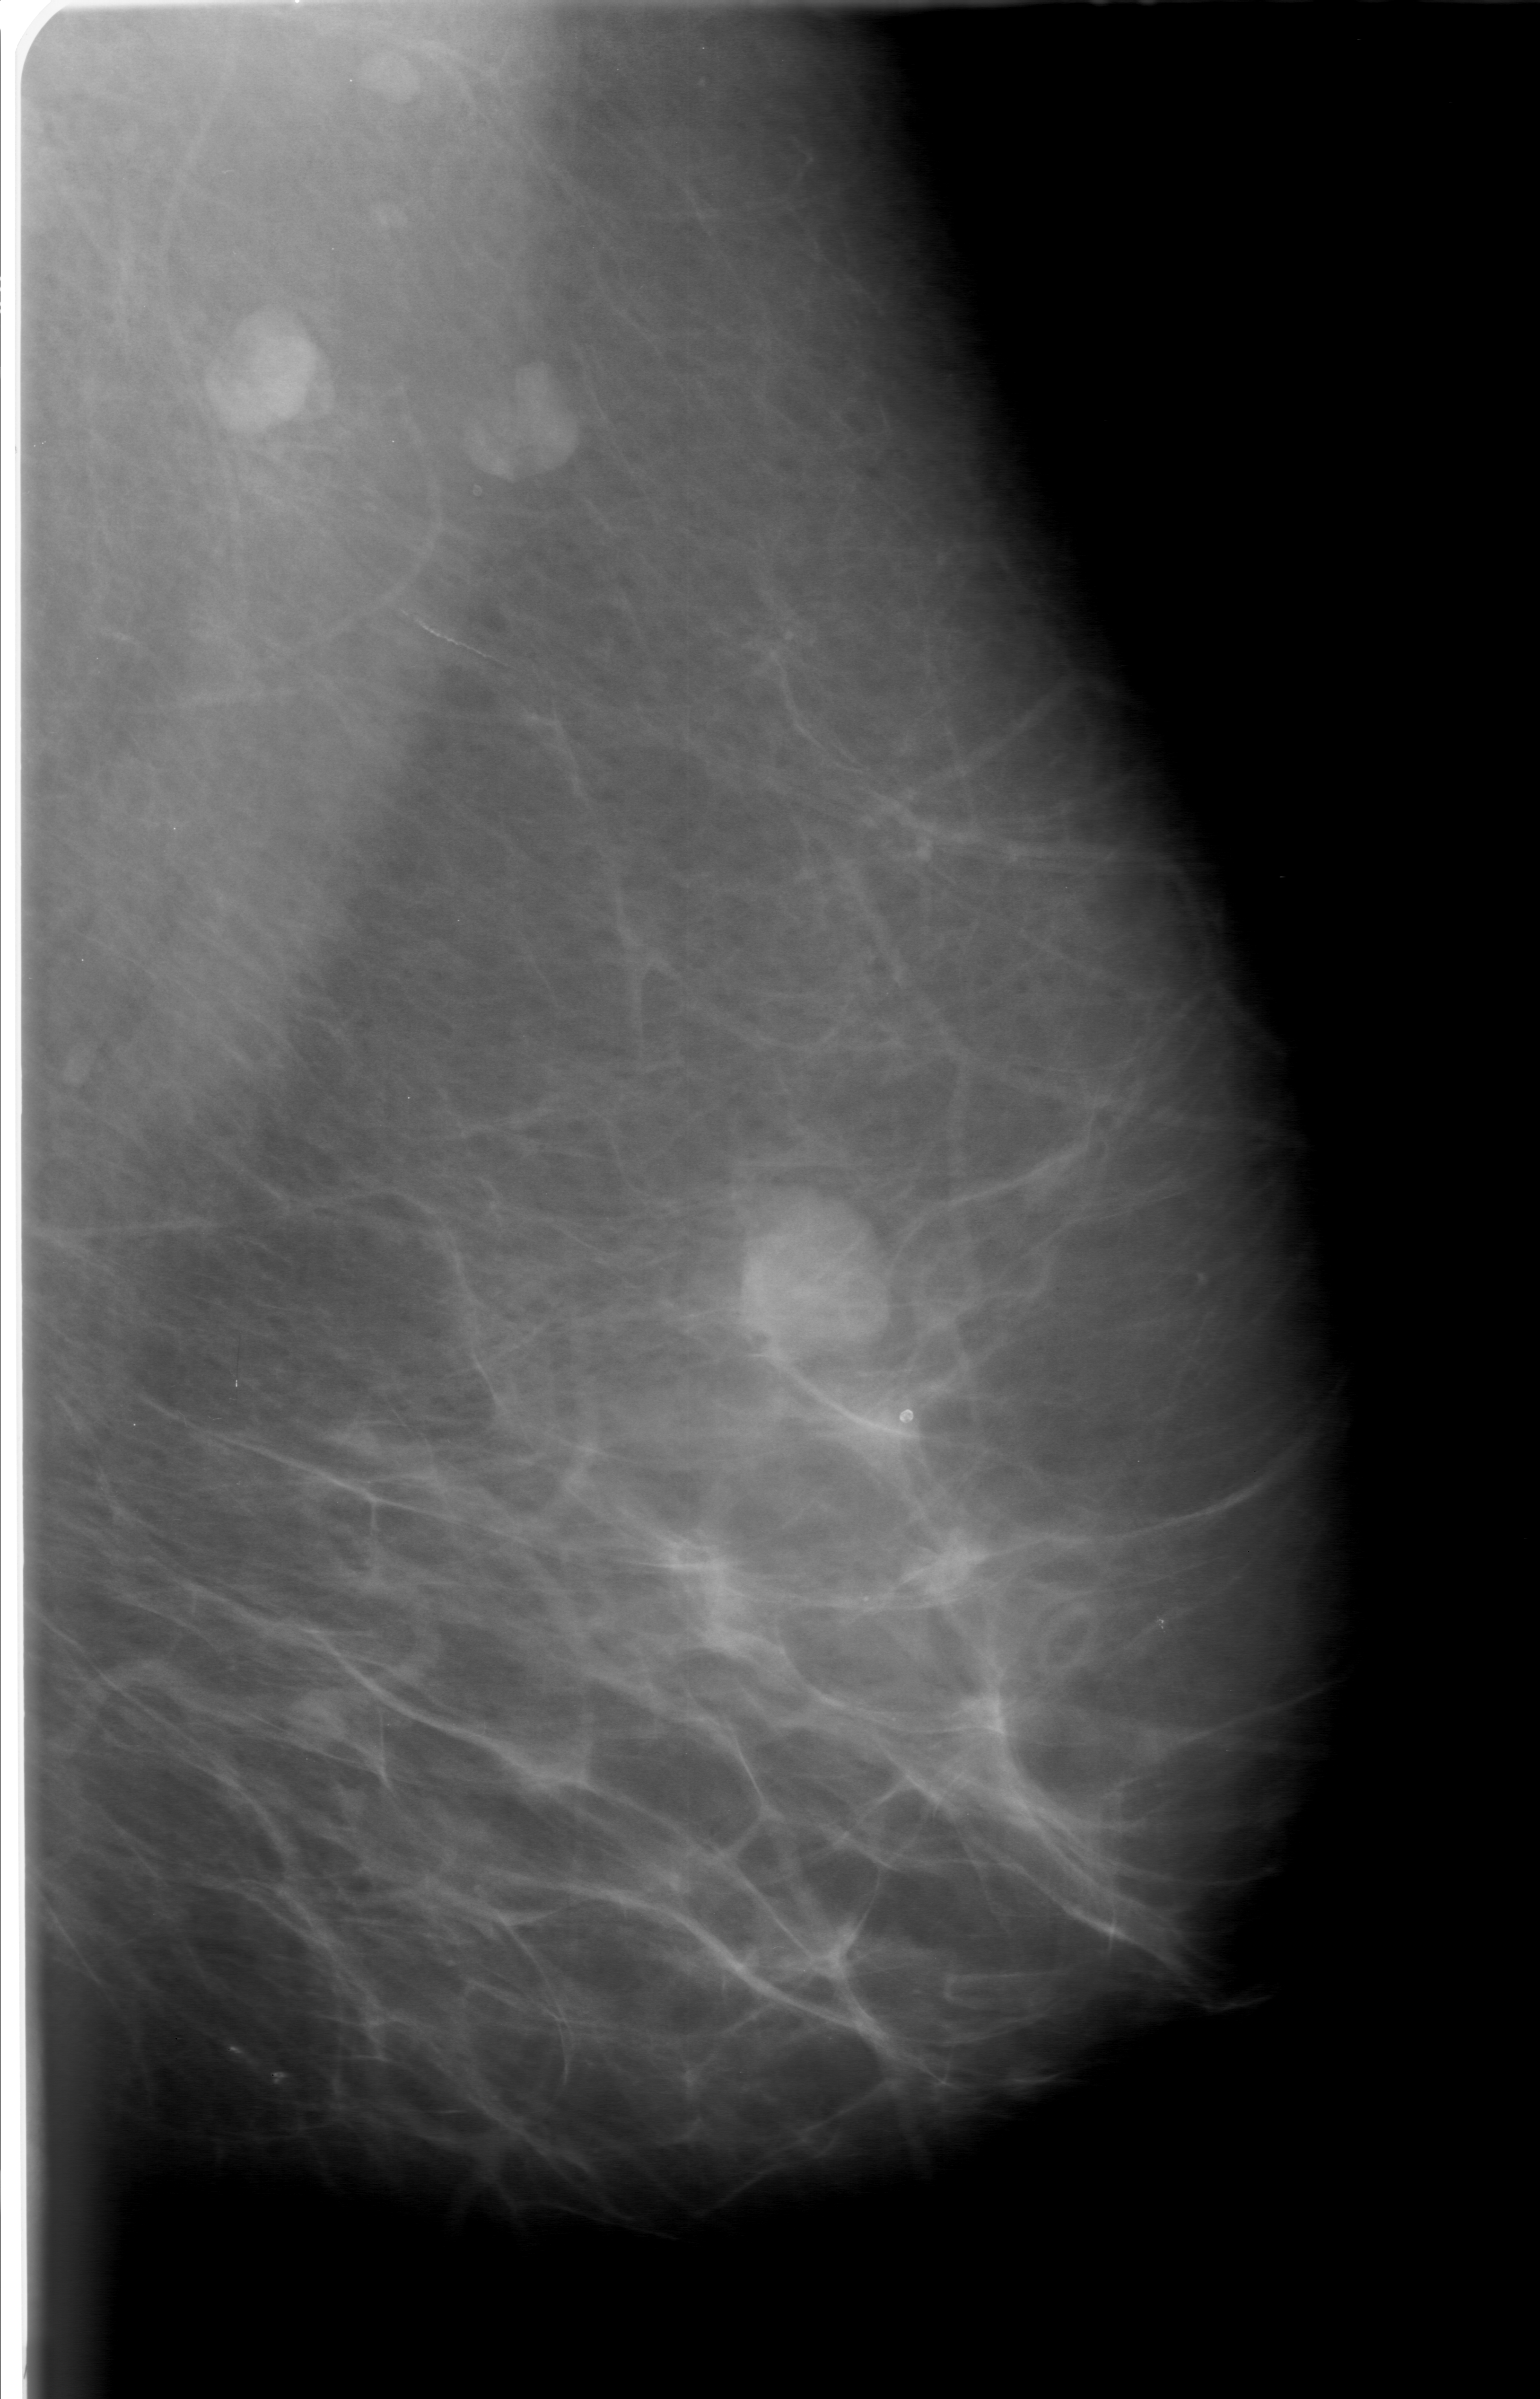
Scanned film-screen mammogram; left breast; MLO view; BI-RADS breast density category 1 (scale 1–4).
Finding: mass, shape lobulated, margins circumscribed; BI-RADS assessment category 0; pathology result (as recorded, not read from the image): benign.